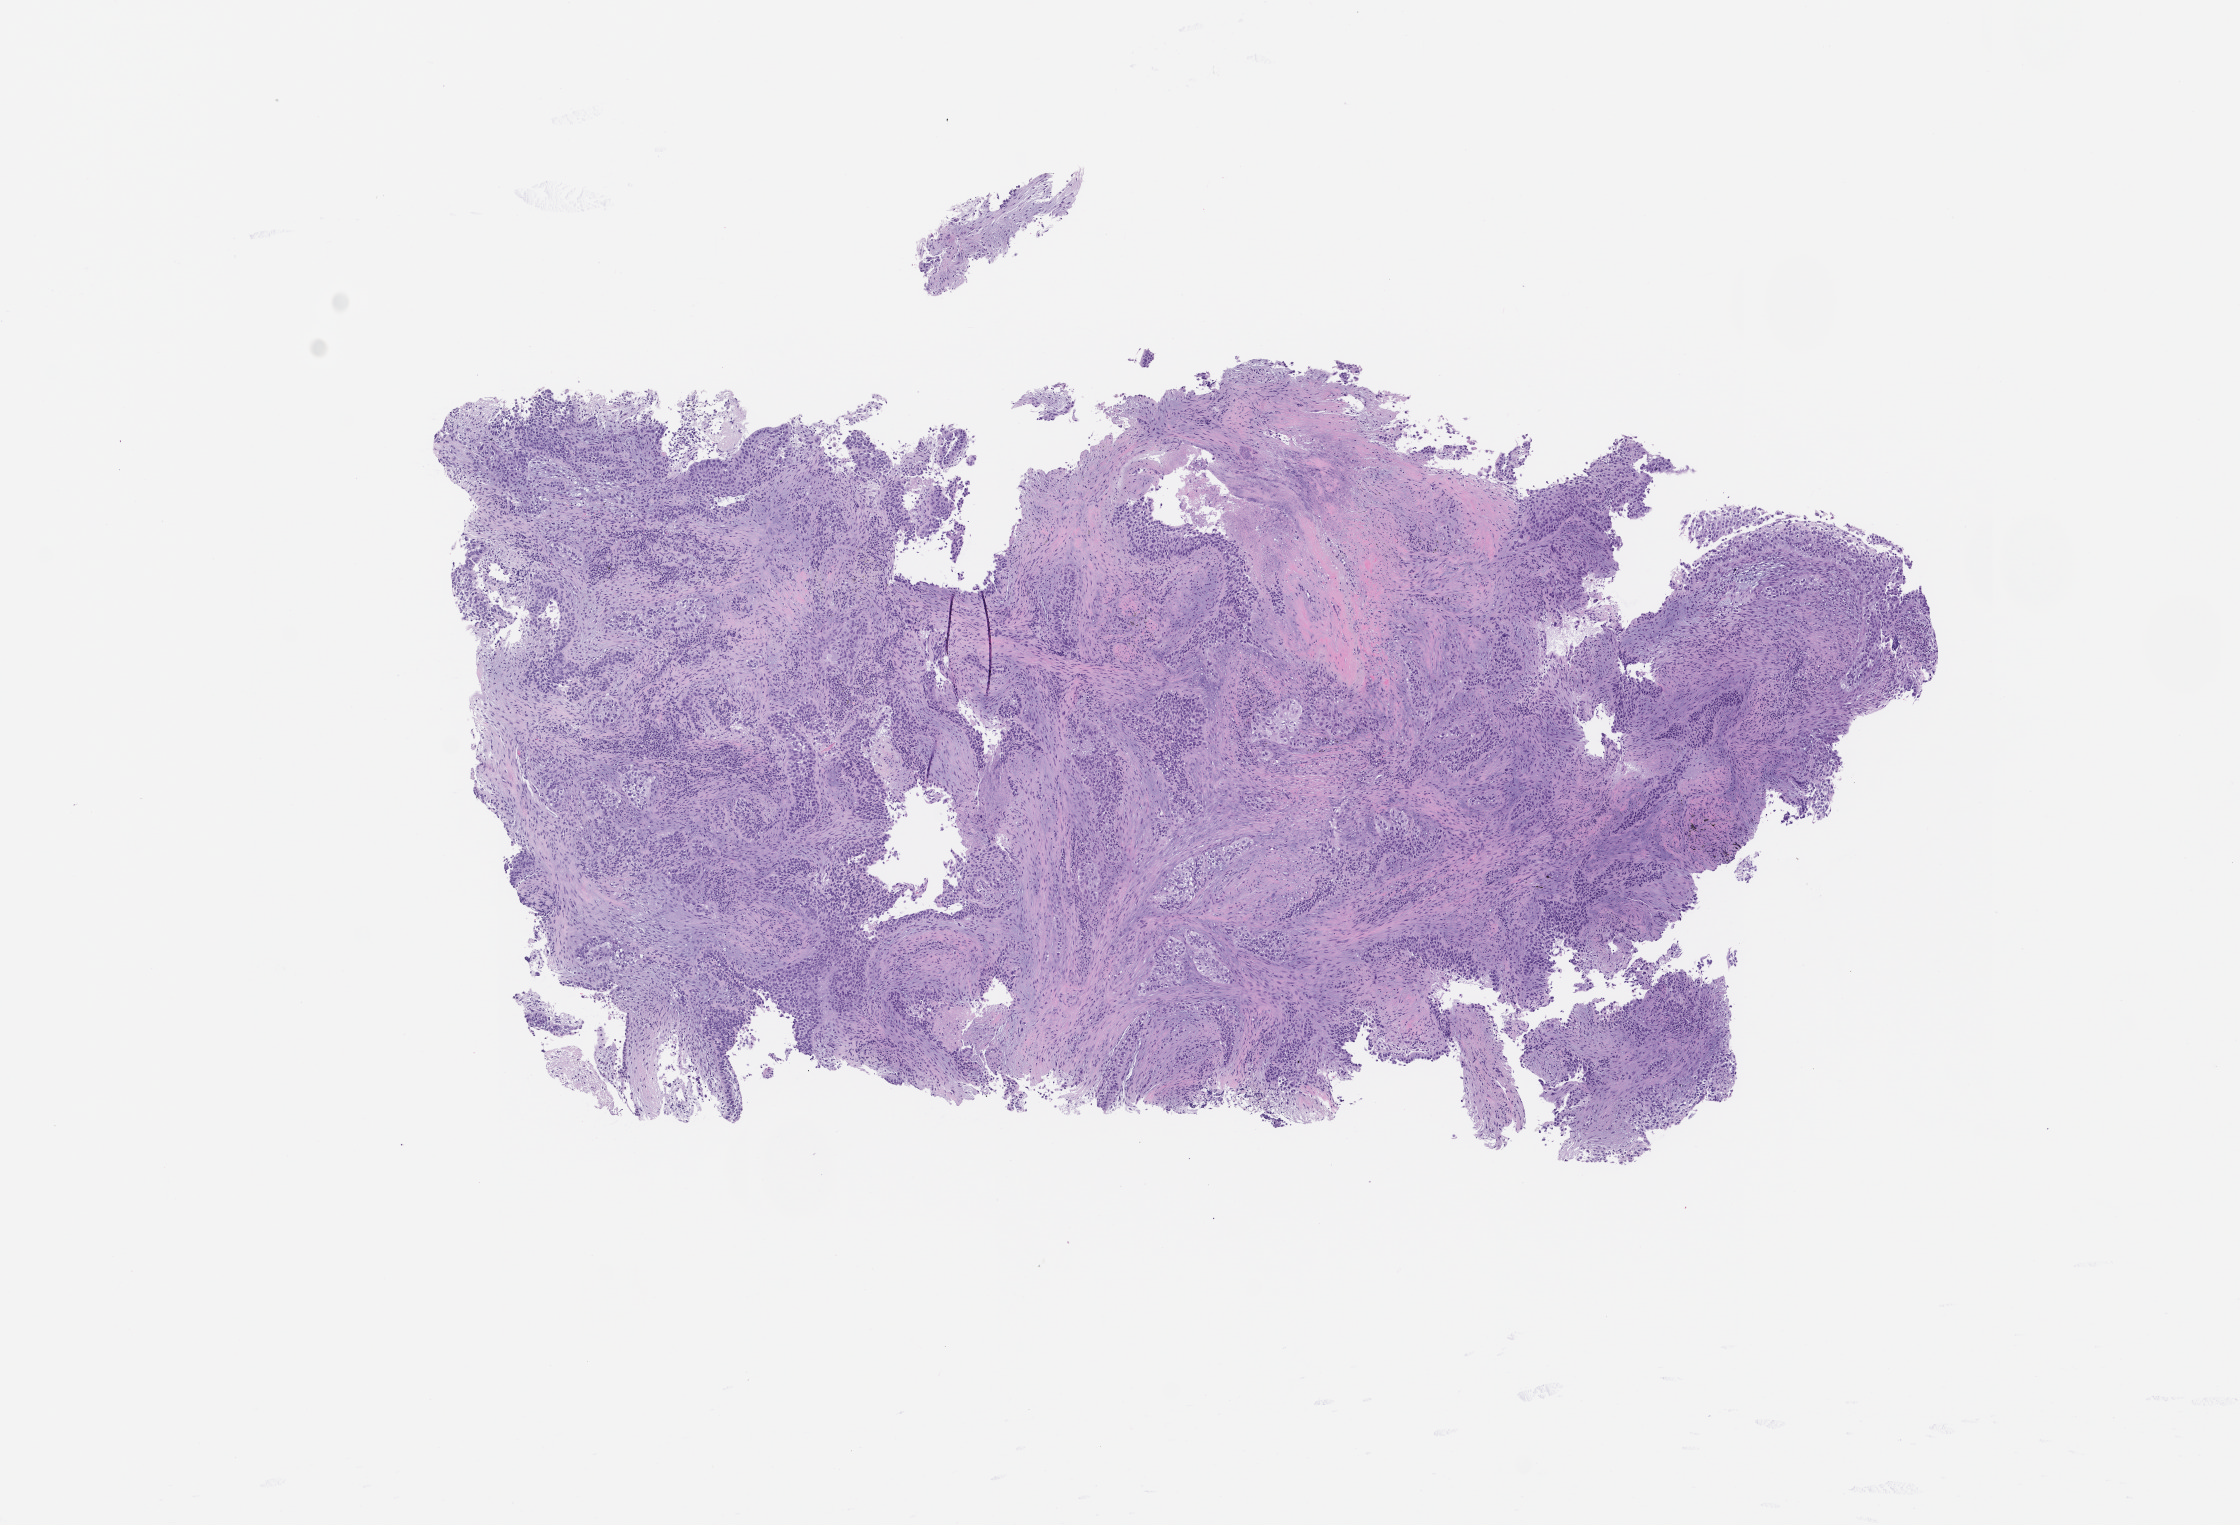
Whole-slide image, H&E stain of the patient's (originator) tumor tissue, low-resolution overview of the scanned area, about 9.0 x 6.1 mm; FFPE section; tumor site category: lung. Patient female; aged 66.
- diagnosis: Lung Squamous Cell Carcinoma